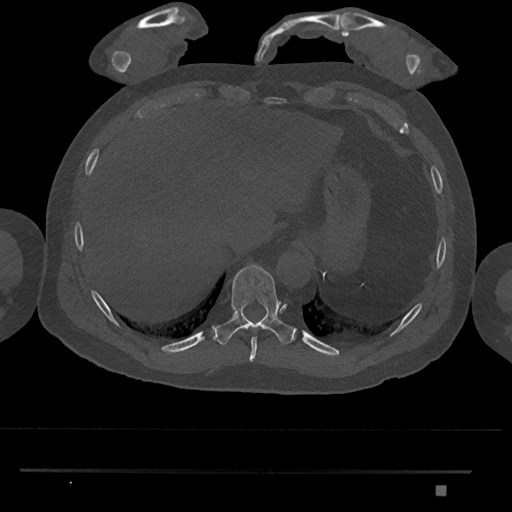
CT including the spine, one axial slice. Slice 1011 of 1134 in the series (ordered by position). Bone window (W 1800 / L 400 HU). 512 × 512 image matrix. Patient: male, 65 years. From the clinical record (not read from this slice): primary cancer: prostate.
Outlined on this slice (semi-automatic segmentation, software-assisted and operator-edited):
- T10 vertebra: bounding box [x1, y1, x2, y2] px = [212, 264, 295, 345]
- T9 vertebra: [249, 337, 257, 362]